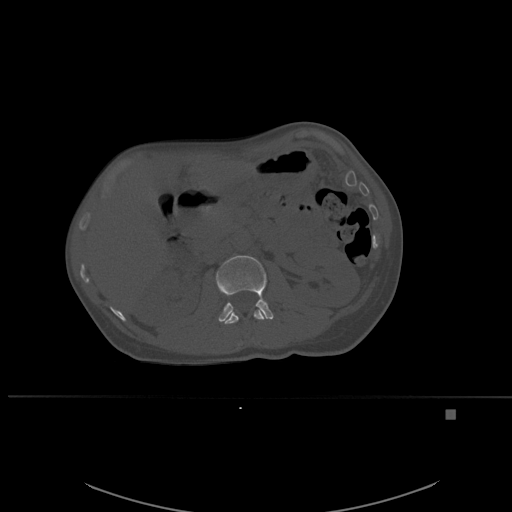
CT including the spine, one axial slice; slice 245 of 537 in the series (ordered by position); bone window (W 1800 / L 400 HU); 512 × 512 image matrix. Female patient, age 45 years. From the clinical record (not read from this slice): primary cancer: lung.
Annotated regions visible in this slice (semi-automatically segmented with operator editing):
- L1 vertebra: bounding box <222,309,265,325> (left, top, right, bottom; pixels)
- L2 vertebra: <216,255,274,322>